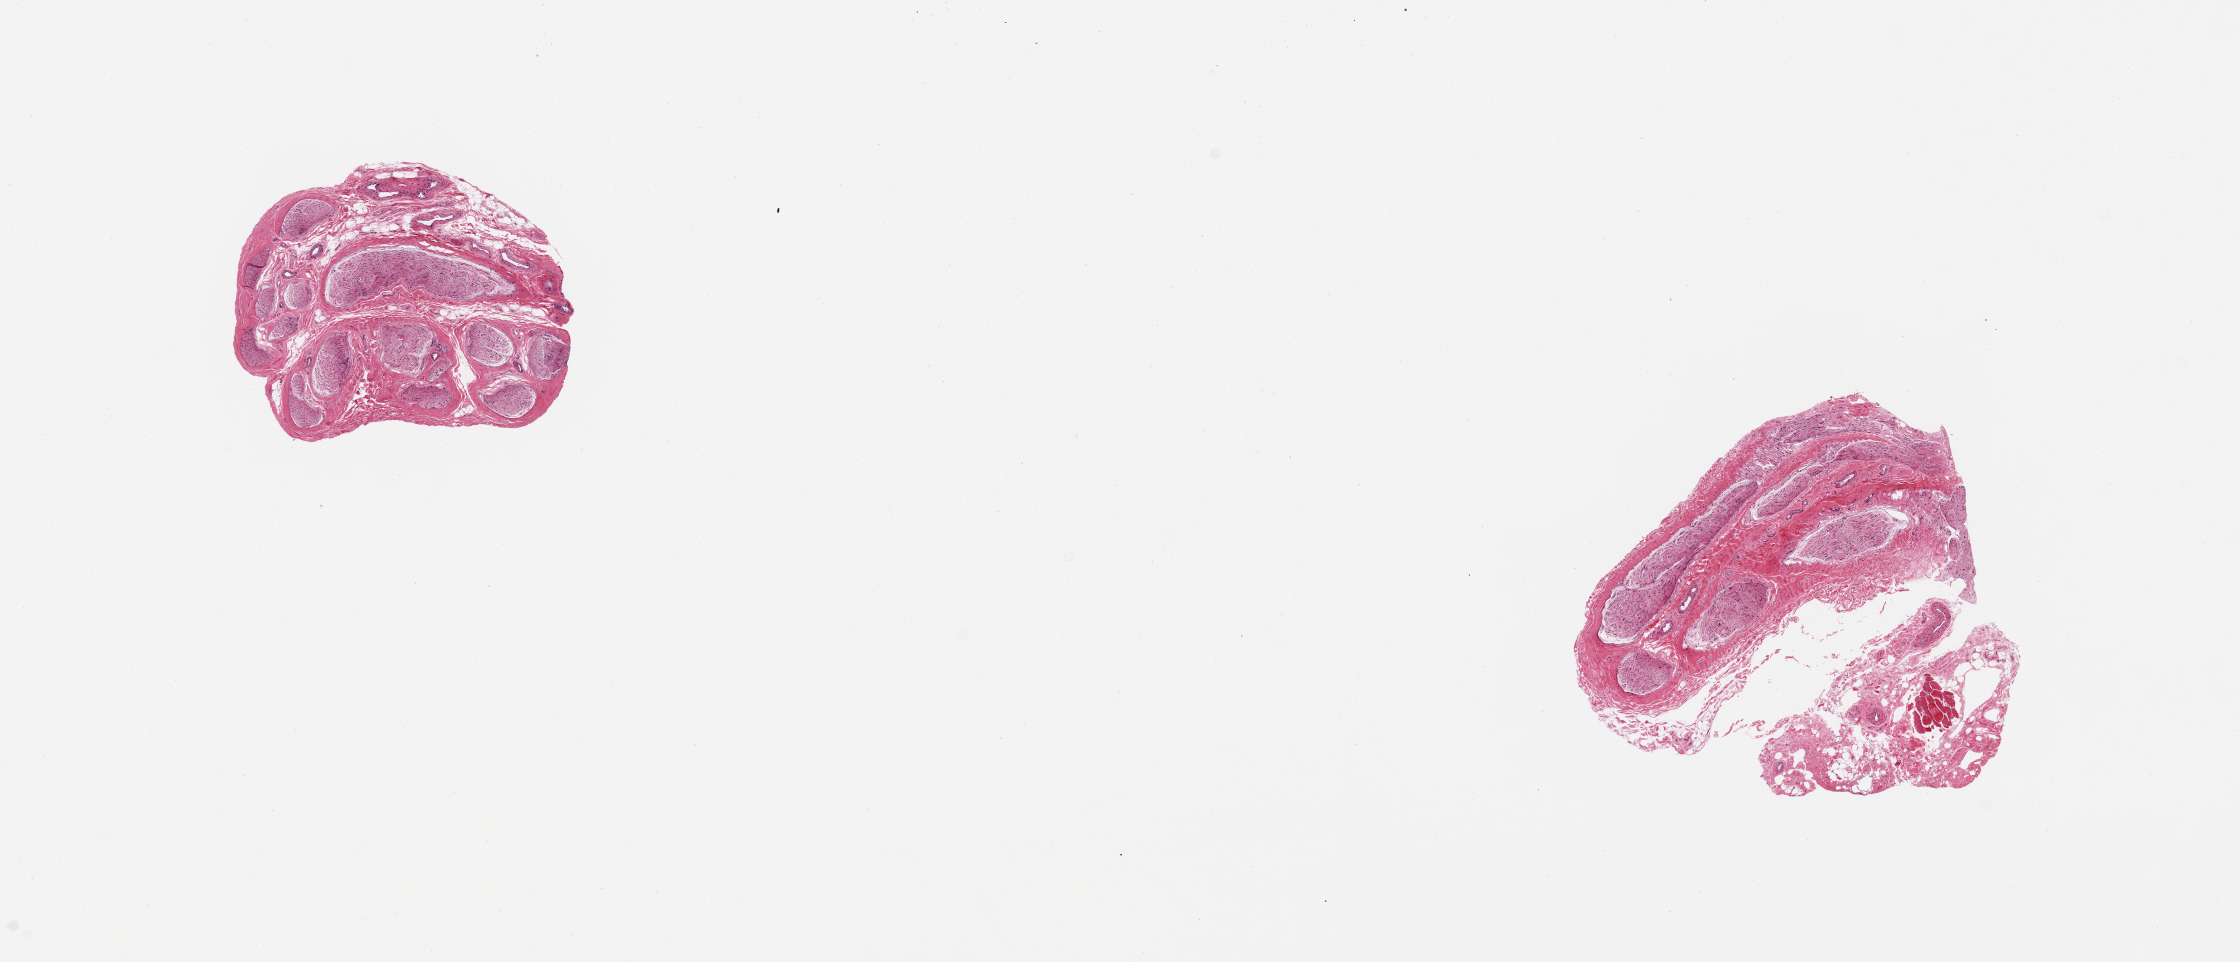
Whole-slide image, hematoxylin and eosin (H&E) stain, brightfield — whole scanned area (about 17.7 x 7.6 mm, acquisition: 20x scan) shown as a low-resolution overview, PAXgene-fixed paraffin-embedded (PFPE) section, target tissue: tibial nerve, donor tissue sample. Donor: male.
Reviewer comment on this tissue sample: 2 pieces: ~10% internal/external fat; small skeletal muscle fragment.